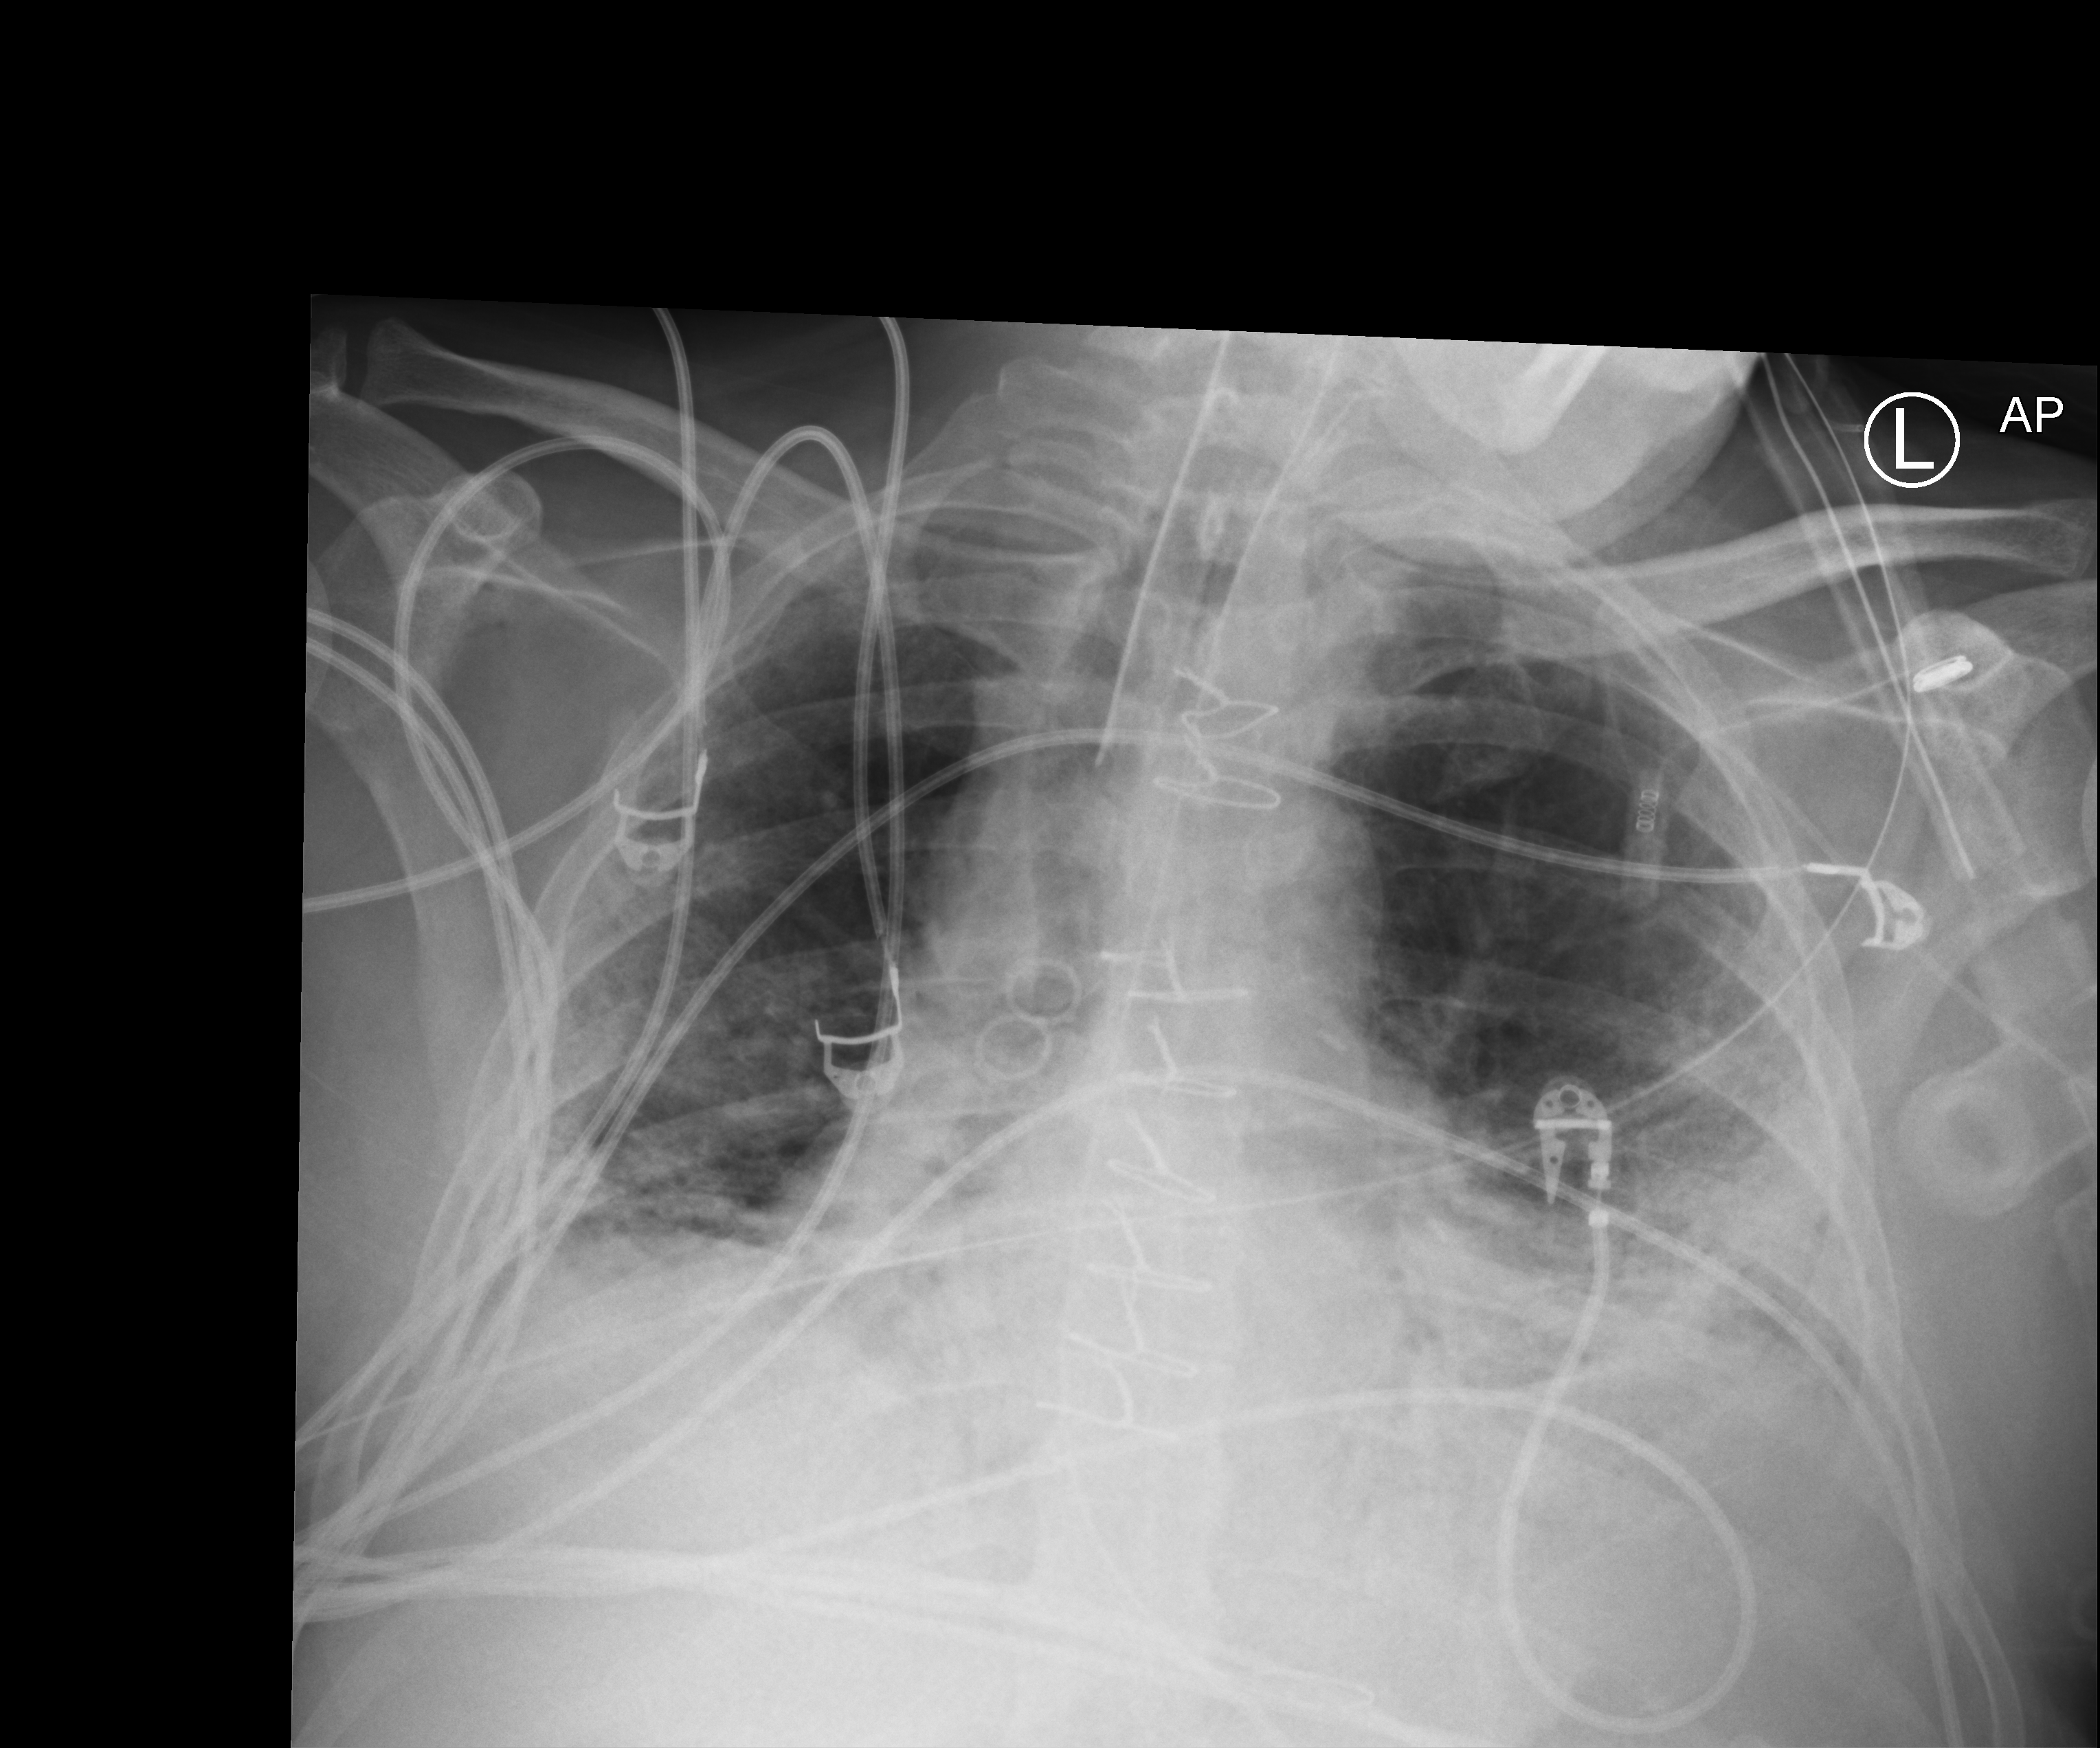
Bedside chest radiograph (computed radiography); anteroposterior (AP) projection. Patient hospitalised with COVID-19; male, aged 18–59 years.
From the hospital-stay record, not from the radiograph (when in the stay this image was taken is not recorded):
- admitted to intensive care during this hospital stay: yes
- mechanically ventilated during this hospital stay: yes